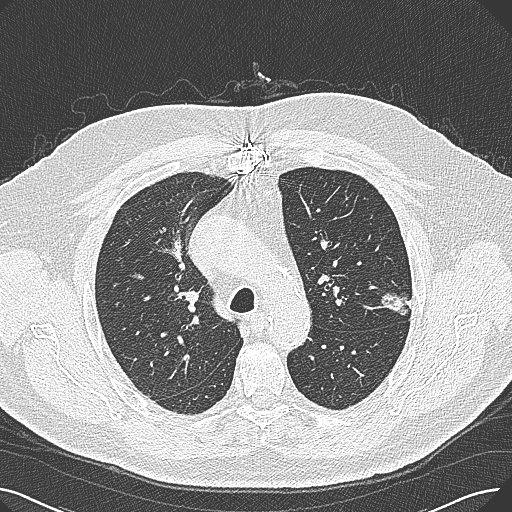
Chest CT (low-dose screening protocol), one axial image. First (baseline) screen. Lung window (W 1500 / L -600 HU). 120 kVp. 512 × 512 image matrix. Male participant, aged 74 years at enrolment. Former smoker at enrolment.
Expert-annotated lung lesion, bounding box <371,273,425,321> (left, top, right, bottom; pixels). The exam's reader record, not a measurement of the box and not confirmed to be the same lesion: non-calcified nodule or mass ≥4 mm, left upper lobe, 15 × 10 mm, poorly defined margins, soft tissue attenuation. Official screen result: positive, change unspecified: nodule(s) >= 4 mm or enlarging nodule(s), mass(es), or other non-specific abnormalities suspicious for lung cancer. Participant outcome: lung cancer diagnosed 124 days after this screen — adenocarcinoma, NOS, left upper lobe, well differentiated (G1), stage IA (AJCC 6th edition), 26 mm at pathology.